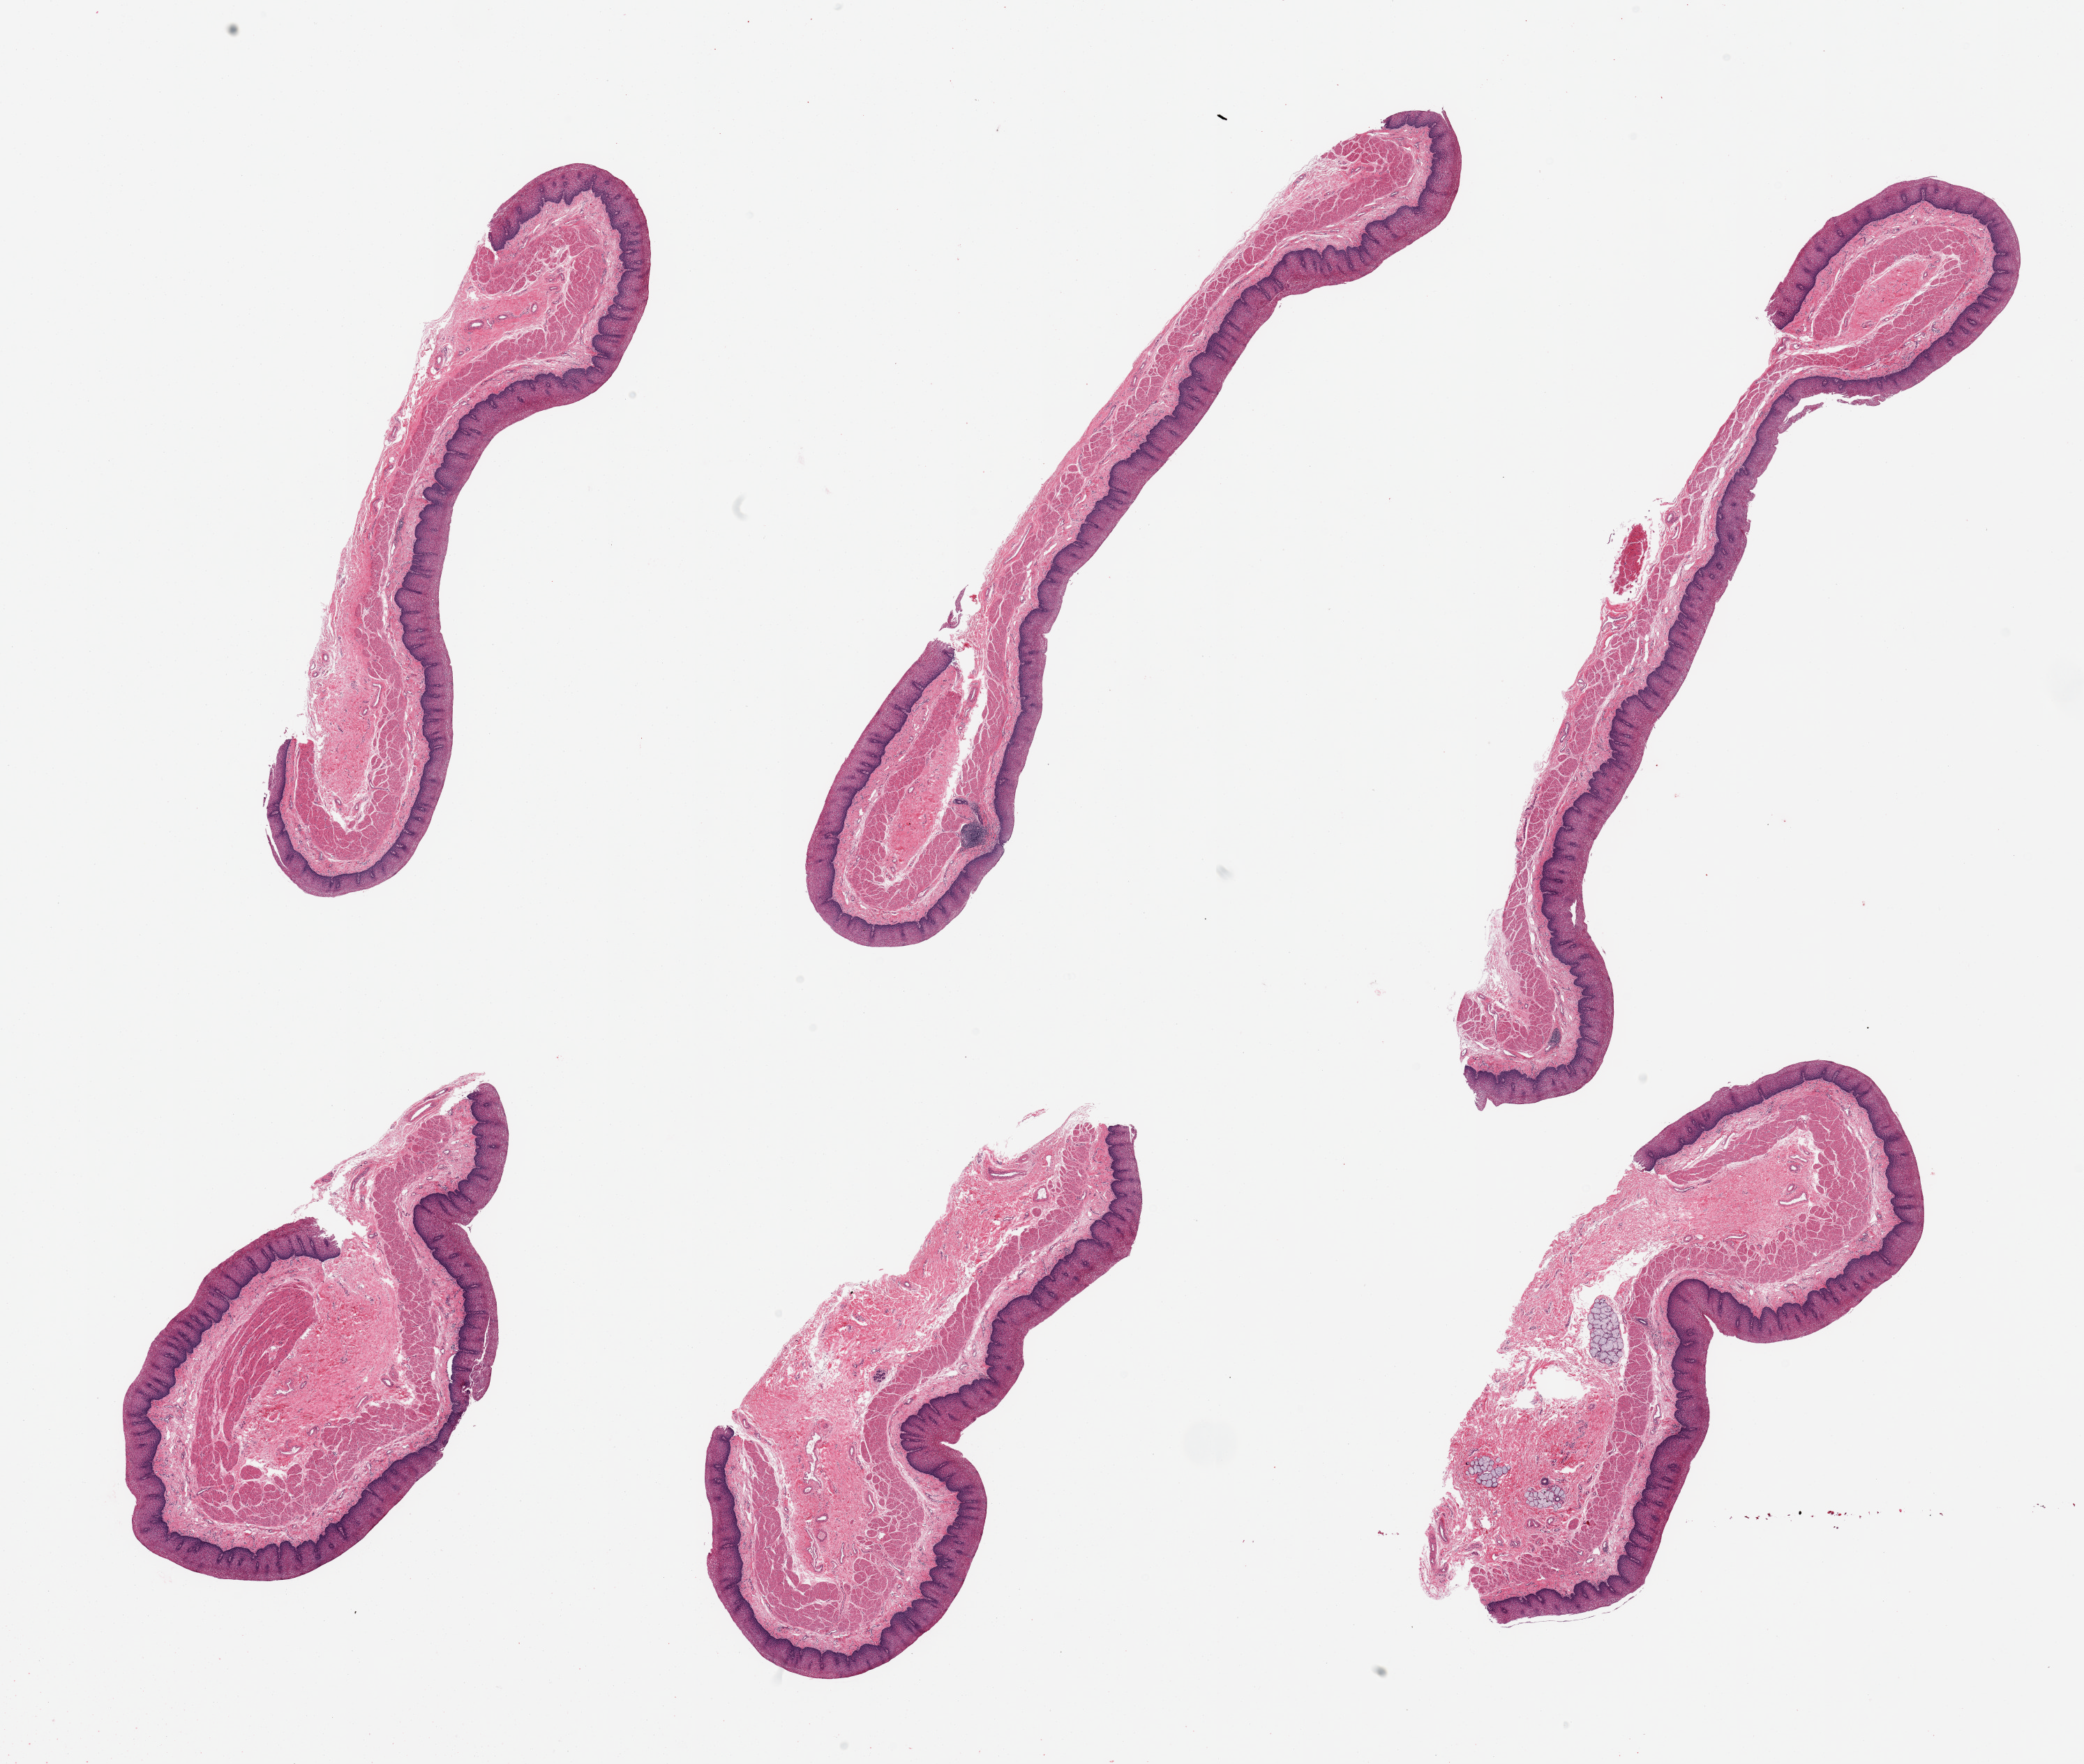
Hematoxylin and eosin (H&E) whole-slide image, whole scanned area (about 23.6 x 20.0 mm, from a 20x scan) shown as a low-resolution overview; PAXgene-fixed paraffin-embedded (PFPE) section; sampled site (target tissue): esophageal mucous membrane; tissue donor sample. Female donor.
Pathologist's review note for this sample: 6 pieces, squamous mucosa is ~0.3-0.4mm, ~25-50% thickness.